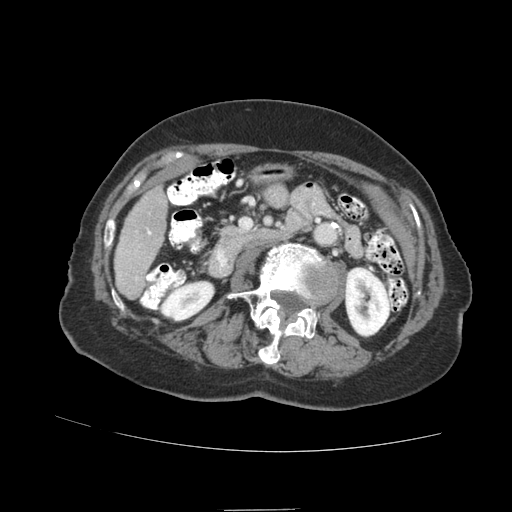
Contrast-enhanced abdominal CT (liver protocol), one axial slice; position 22 of 89 along the scan axis; reconstruction kernel STANDARD; soft-tissue window (W 400 / L 40 HU); 2.5 mm slice thickness; 512 × 512 image matrix, field of view 360 × 360 mm. Case-level facts recorded for this patient, not image findings: diagnosis: hepatocellular carcinoma (patient treated with transarterial chemoembolisation; whether this scan precedes or follows treatment is not stated here); TNM stage (as recorded): Stage-II.
Structures marked on this image (semi-automatically segmented with operator editing):
- liver parenchyma outside the tumour (the mass and vessels are separate outlines, so this box may not span the whole liver): box from (x=114, y=186) to (x=168, y=300) px
- liver vessels: (x=135, y=229)–(x=151, y=280)